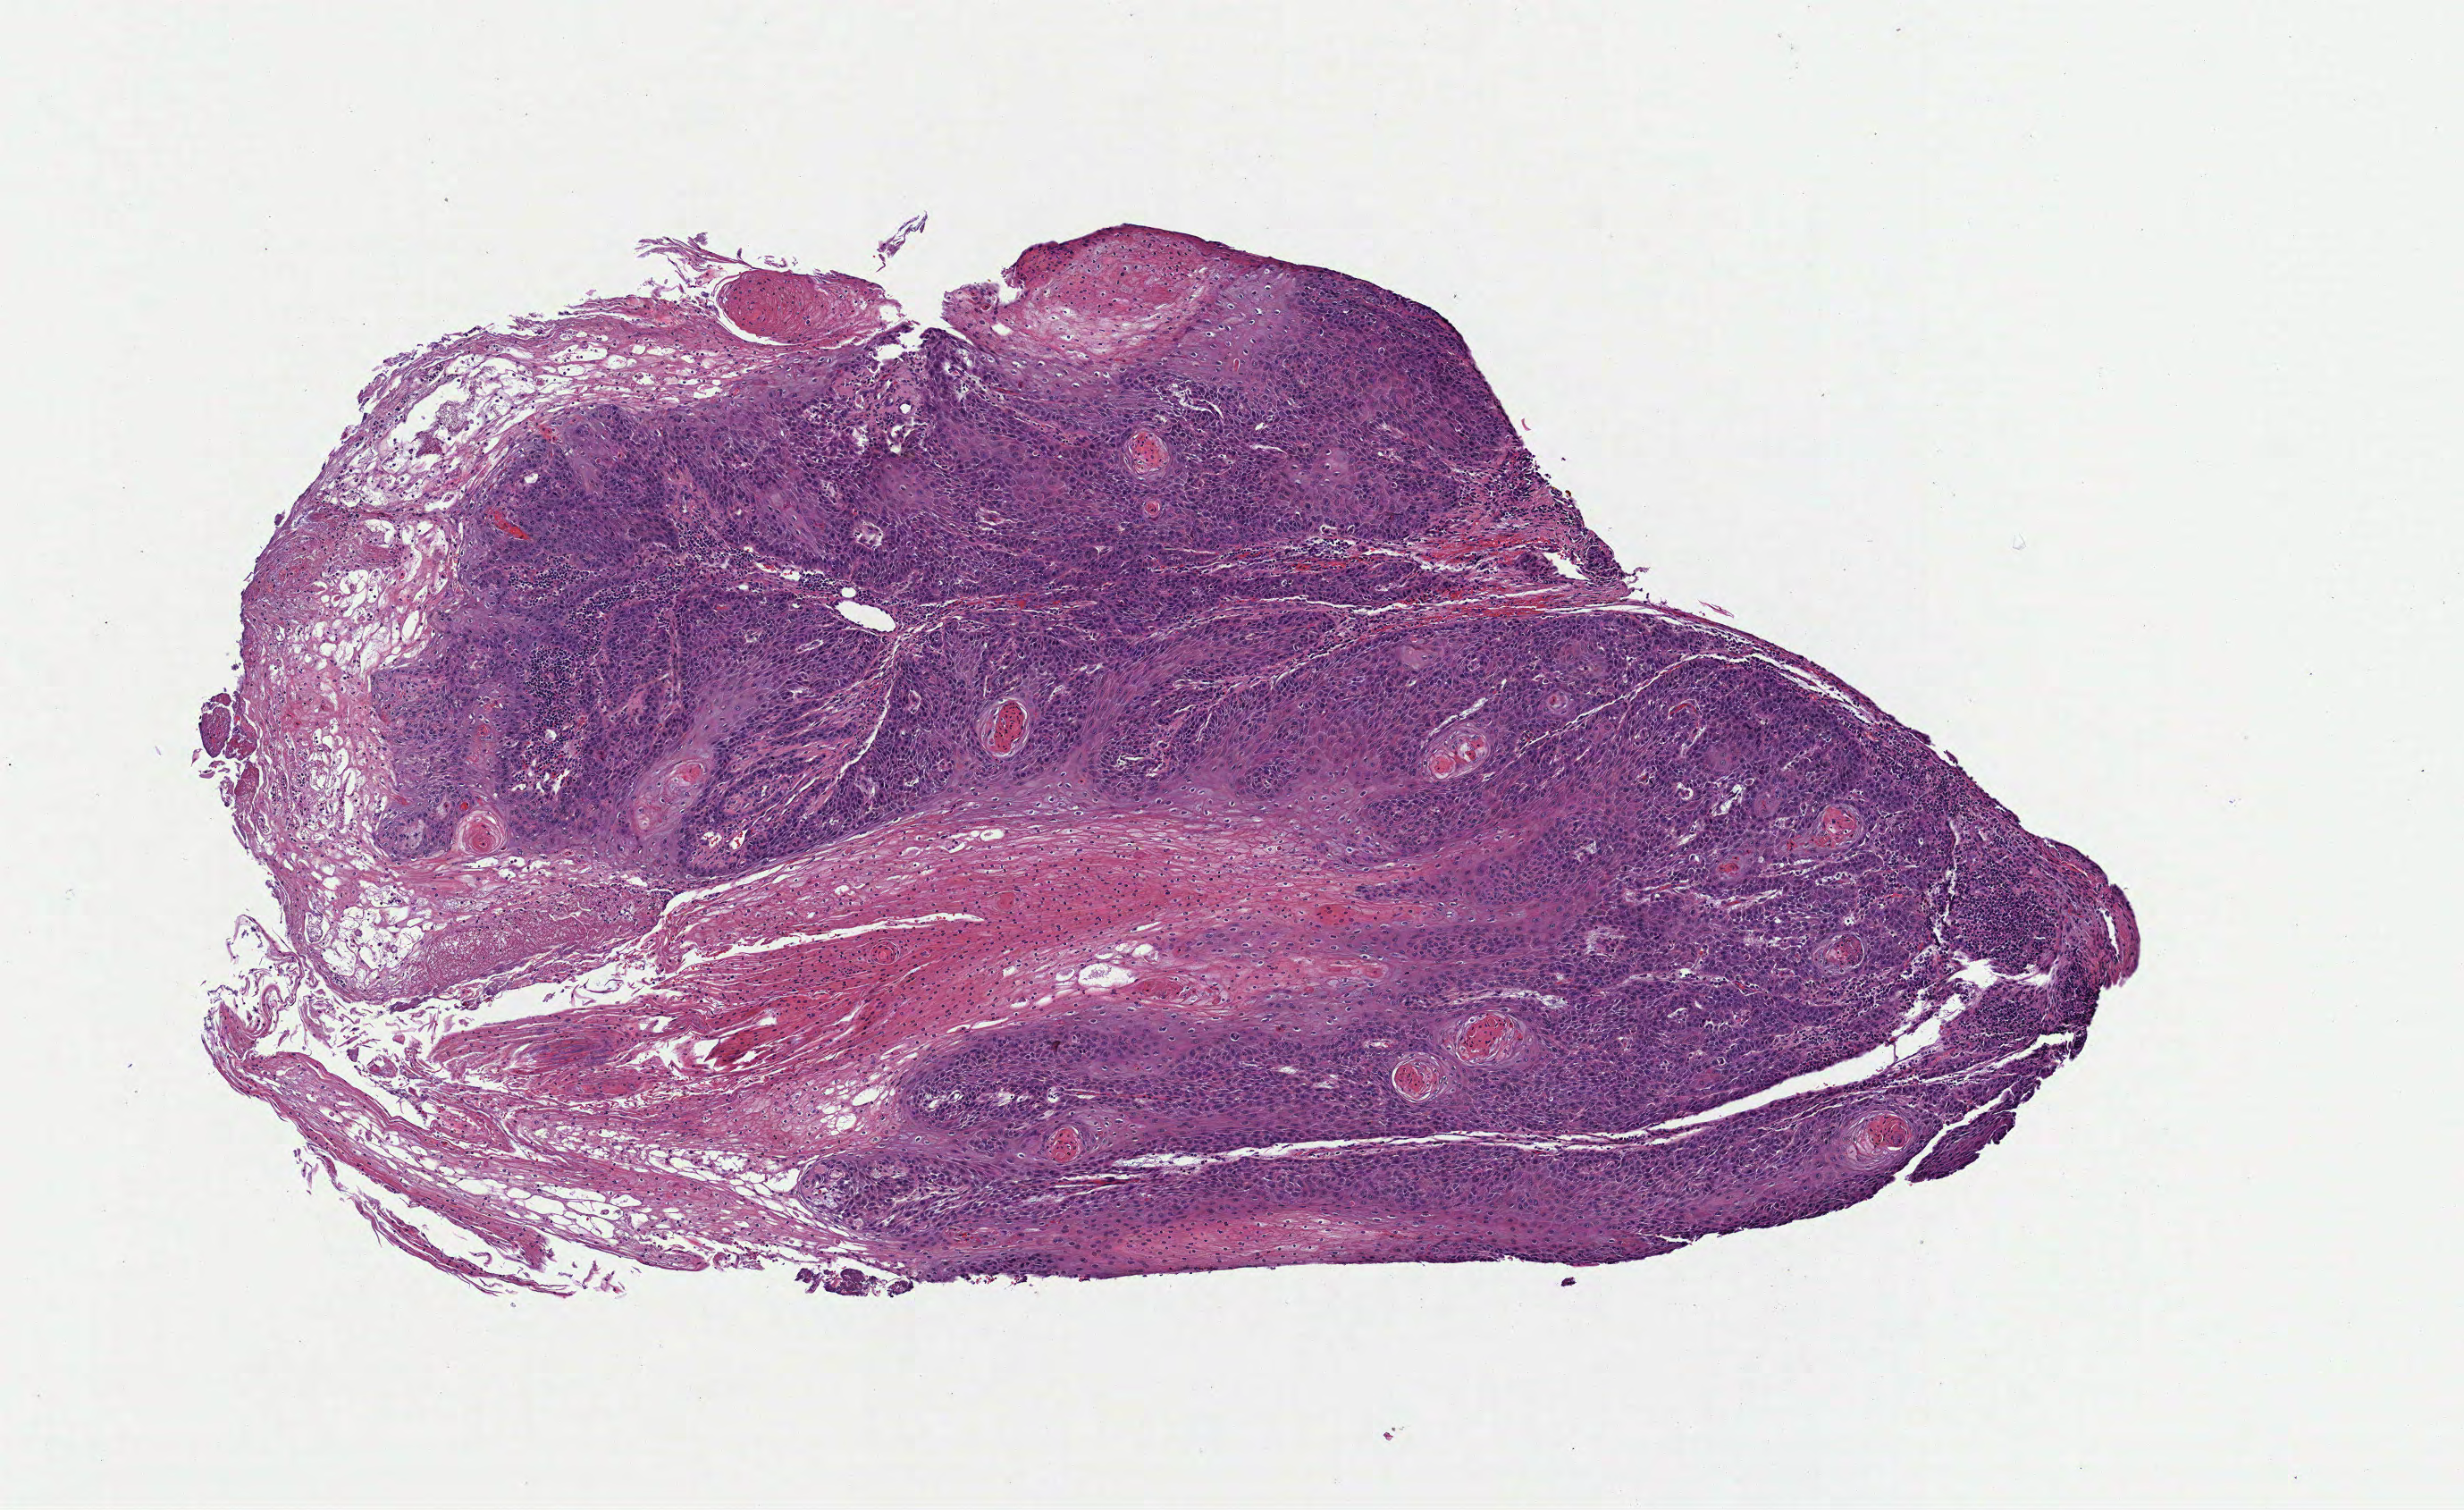
Digitized Hematoxylin and eosin (H&E) stained tissue section (whole slide) — shown as a low-resolution overview of the whole scanned area (about 5.6 x 3.4 mm, slide scanned at 40x). FFPE section. Sample: primary tumour, head and neck. Male, age 56 years at initial diagnosis. Histologic grade: G1 (well differentiated).
Laterality: left. TNM: T4a N1 MX. Pathologic diagnosis: Squamous cell carcinoma, keratinizing, NOS (mouth, NOS). AJCC pathologic stage: IVA (7th edition).